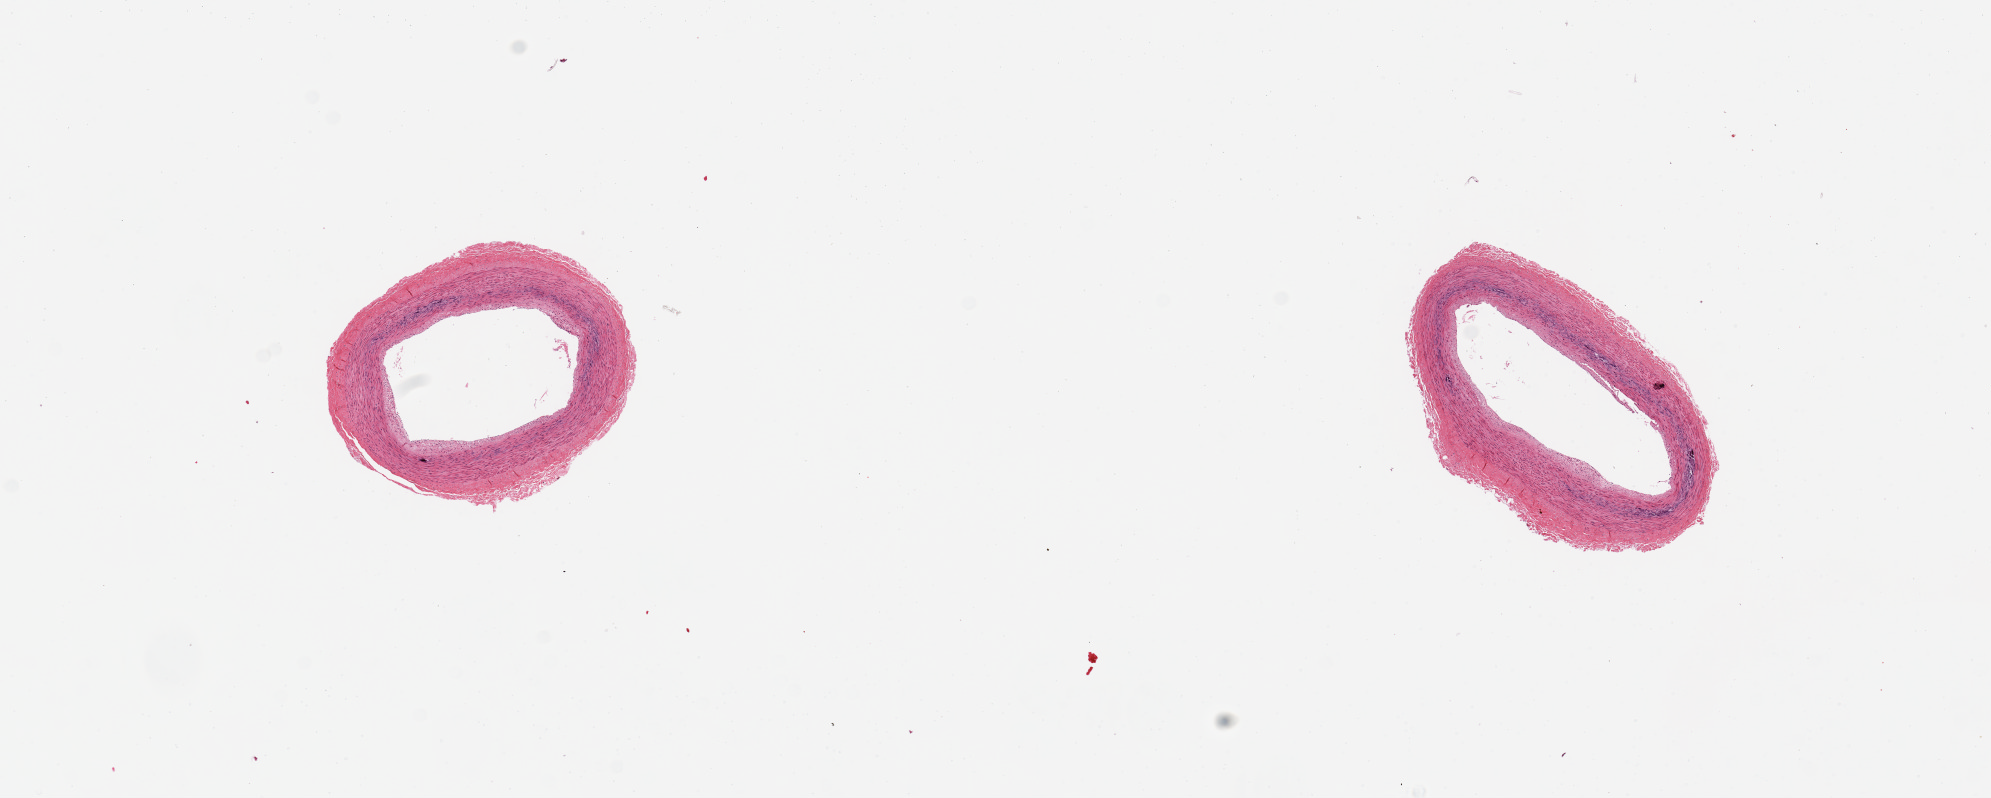
Digitized hematoxylin and eosin (H&E)-stained section, whole scanned area (about 15.8 x 6.3 mm) shown as a low-resolution overview, PAXgene-fixed paraffin-embedded (PFPE) section, sampled site (target tissue): tibial artery, tissue donor sample. Donor: female.
Reviewer comment on this tissue sample: 2 pieces; mild medial calcification; no external fat.